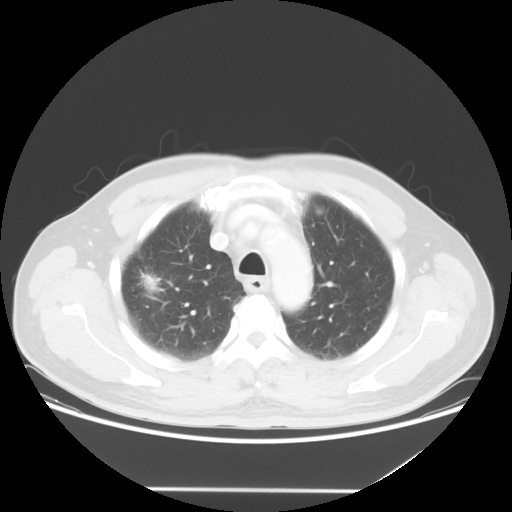
Chest CT, one axial slice; position 41 of 54 along the scan axis; reconstruction kernel STANDARD; 120 kVp; lung window (W 1500 / L -600 HU); 512 × 512 image matrix. Patient: male, 65 years. Case-level facts recorded for this patient, not image findings: clinical TNM (as recorded): T1c N1 M0.
Outlined on this slice (rectangle marked by the reading radiologist):
- lung tumour (recorded histology: adenocarcinoma): bounding box [x1, y1, x2, y2] px = [132, 268, 161, 298]